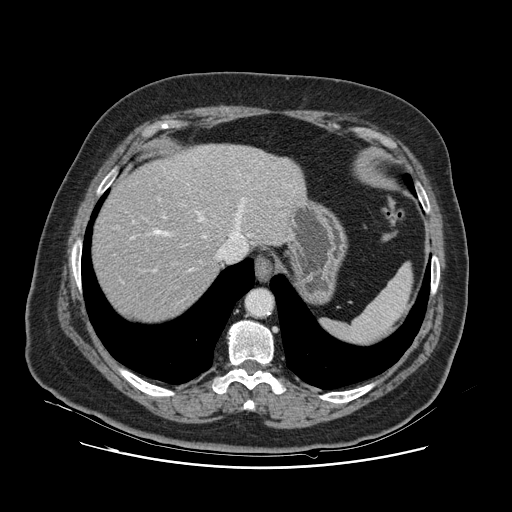
Contrast-enhanced abdominal CT, one axial slice. Position 100 of 132 along the scan axis. 120 kVp. Intravenous contrast given. Soft-tissue window (W 400 / L 40 HU). 2.5 mm slice thickness. 512 × 512 image matrix, field of view 391 × 391 mm. Female patient, age 73 years. Case-level facts recorded for this patient, not image findings: diagnosis: colorectal cancer liver metastases, imaged before liver resection; multiple liver metastases: no; largest metastasis: 7 cm; disease in both lobes: no.
Structures marked on this image (manually delineated by an expert):
- hepatic veins: bounding box (x1, y1, x2, y2) in pixels: (123, 198, 245, 283)
- liver: (93, 145, 303, 322)
- planned liver remnant (the part of the liver to remain after resection): (93, 163, 230, 321)
- portal vein (with intrahepatic branches): (153, 198, 166, 272)